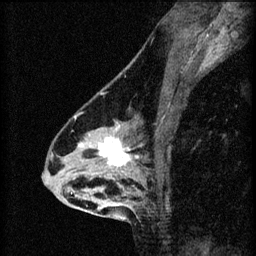
Breast MRI (dynamic contrast-enhanced), one sagittal slice; slice 40 of 60 in the series (ordered by position); 3 images stored at this slice position (order not interpretable as contrast timing); 1.5 T; TE 4.2 ms, TR 8.2 ms; 256 × 256 image matrix, field of view 180 × 180 mm. Female patient, age 46 years.
Structures marked on this image (semi-automatic segmentation, software-assisted and operator-edited):
- analysis volume of interest (the breast-tissue region the enhancement analysis was run in; not a lesion): box from (x=55, y=114) to (x=148, y=209) px
- tumour enhancement mask (voxels above the 70 % enhancement threshold inside the analysis volume of interest): (x=71, y=116)–(x=142, y=197)